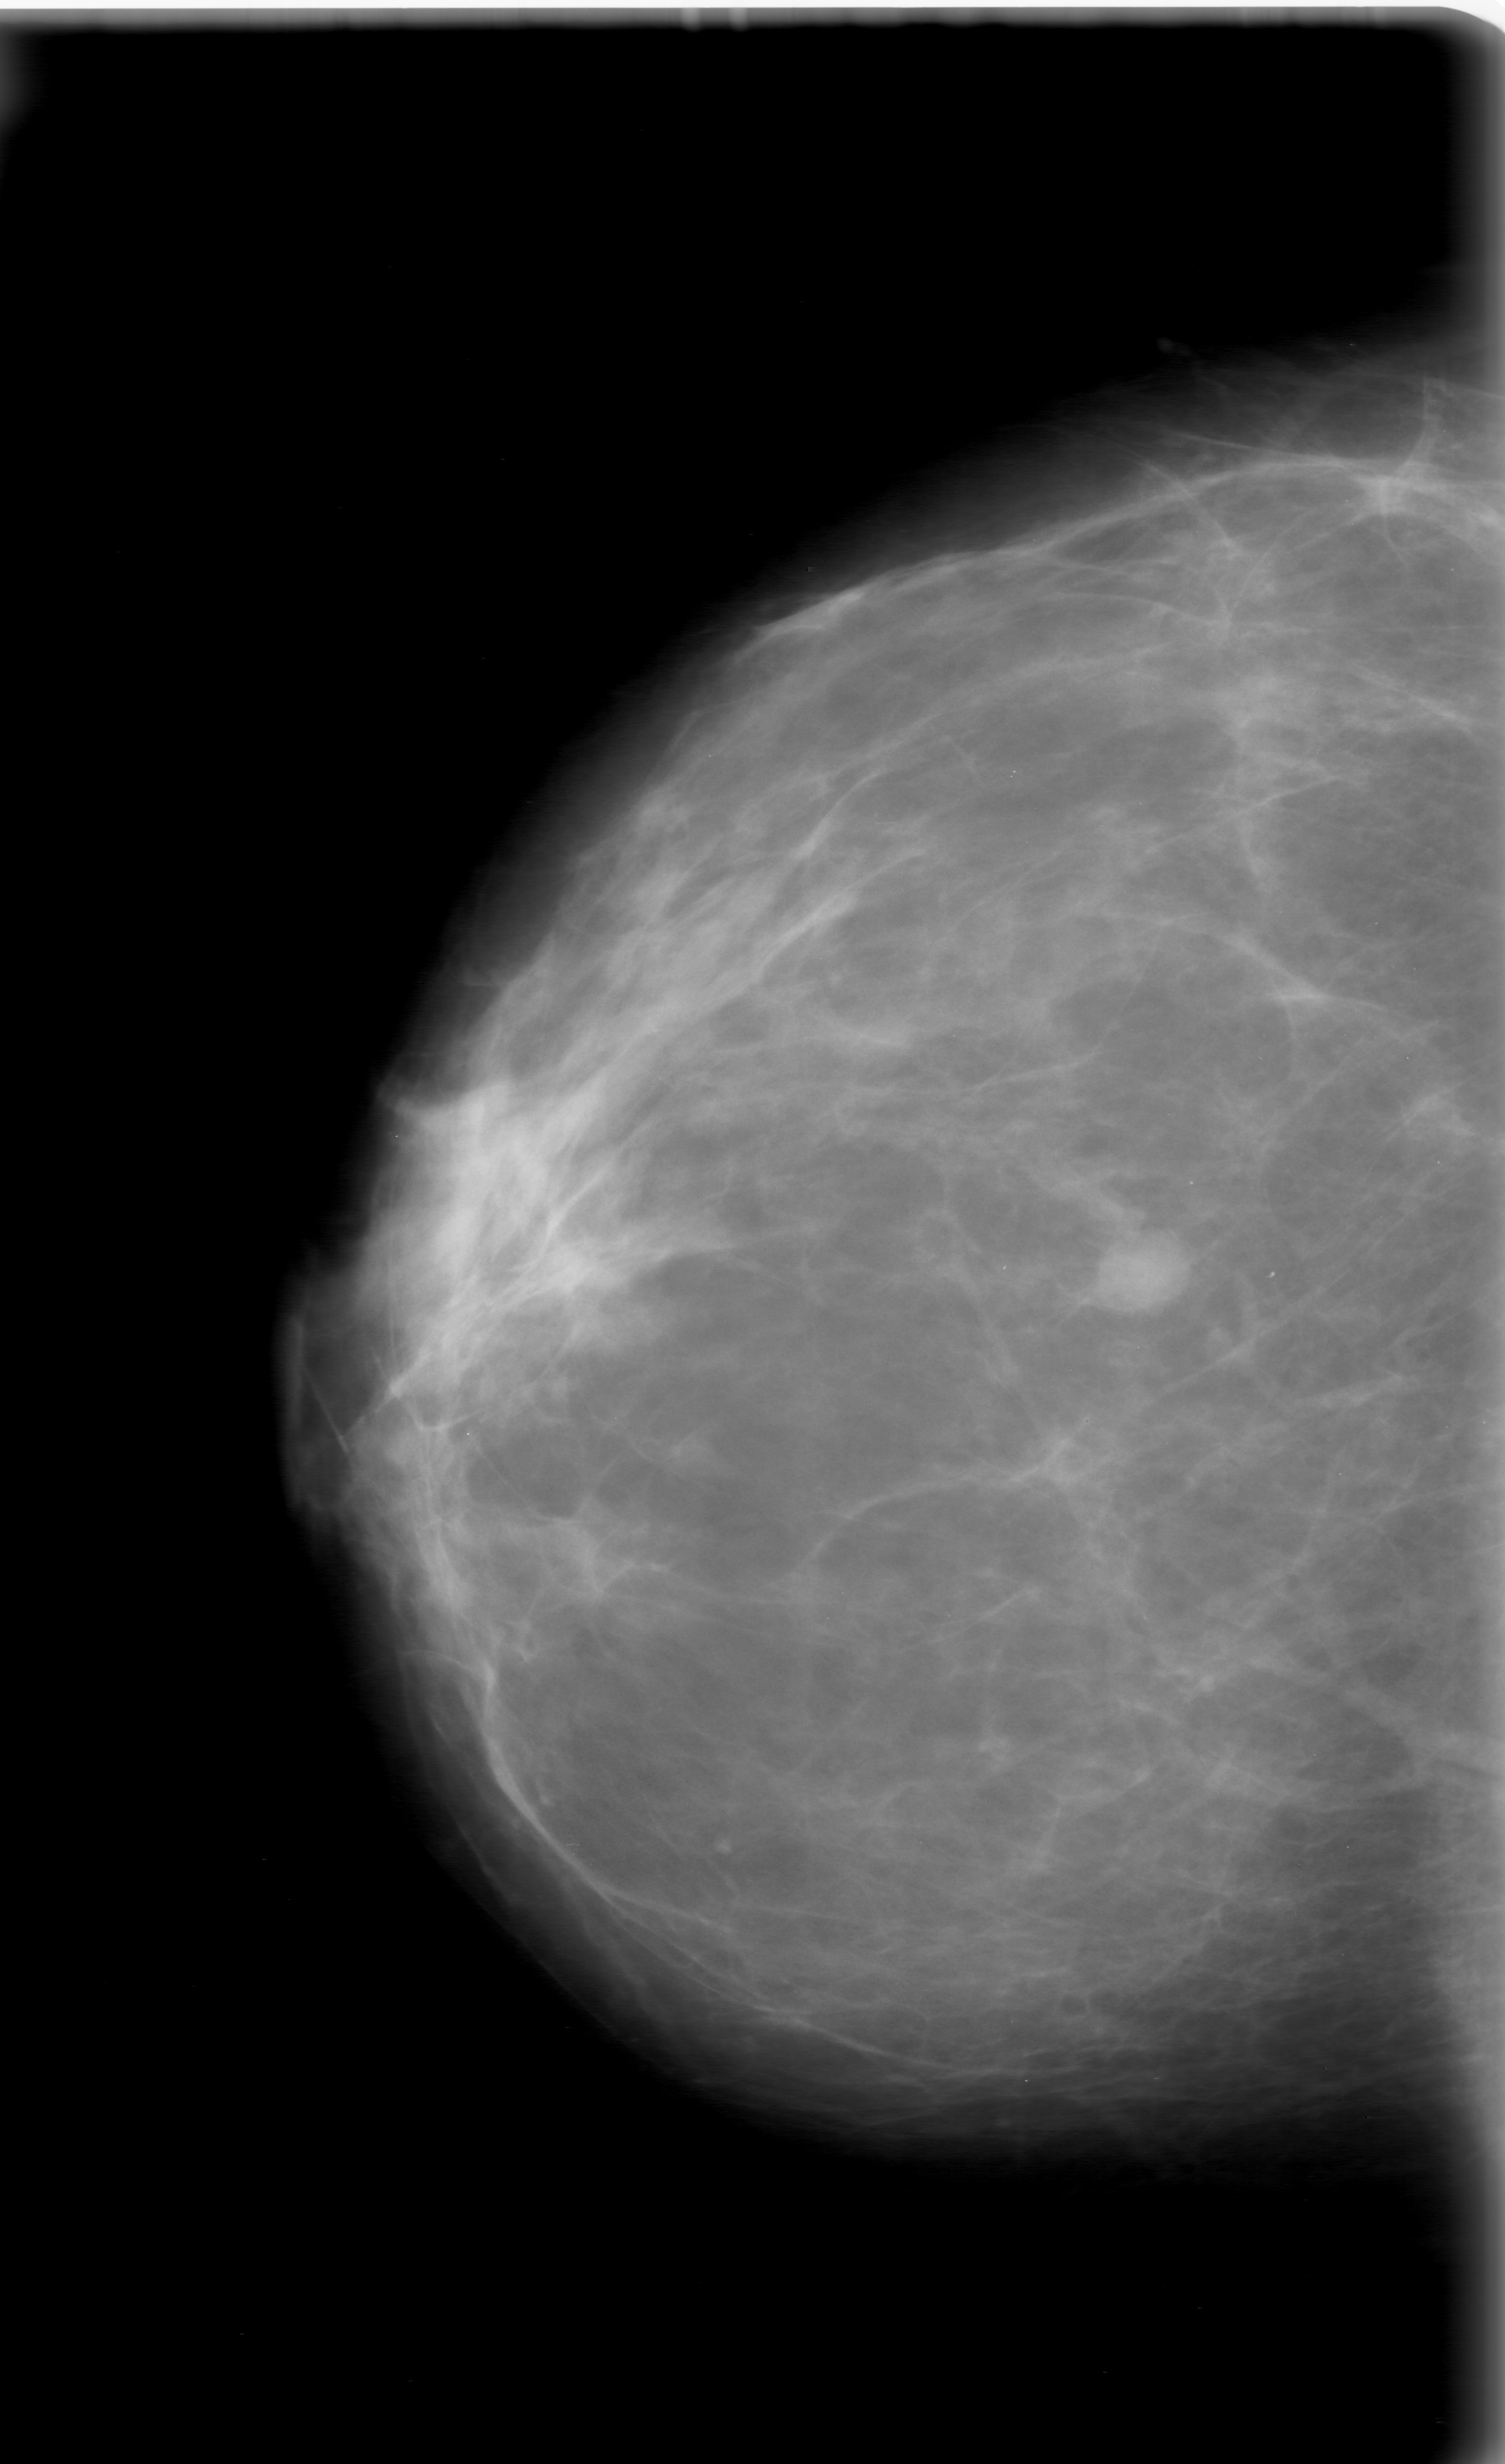
Scanned film-screen mammogram, right breast, craniocaudal (CC) view.
Mass, shape oval, margins ill defined; BI-RADS assessment category 0 (incomplete: needs additional imaging); pathology result (as recorded, not read from the image): benign.